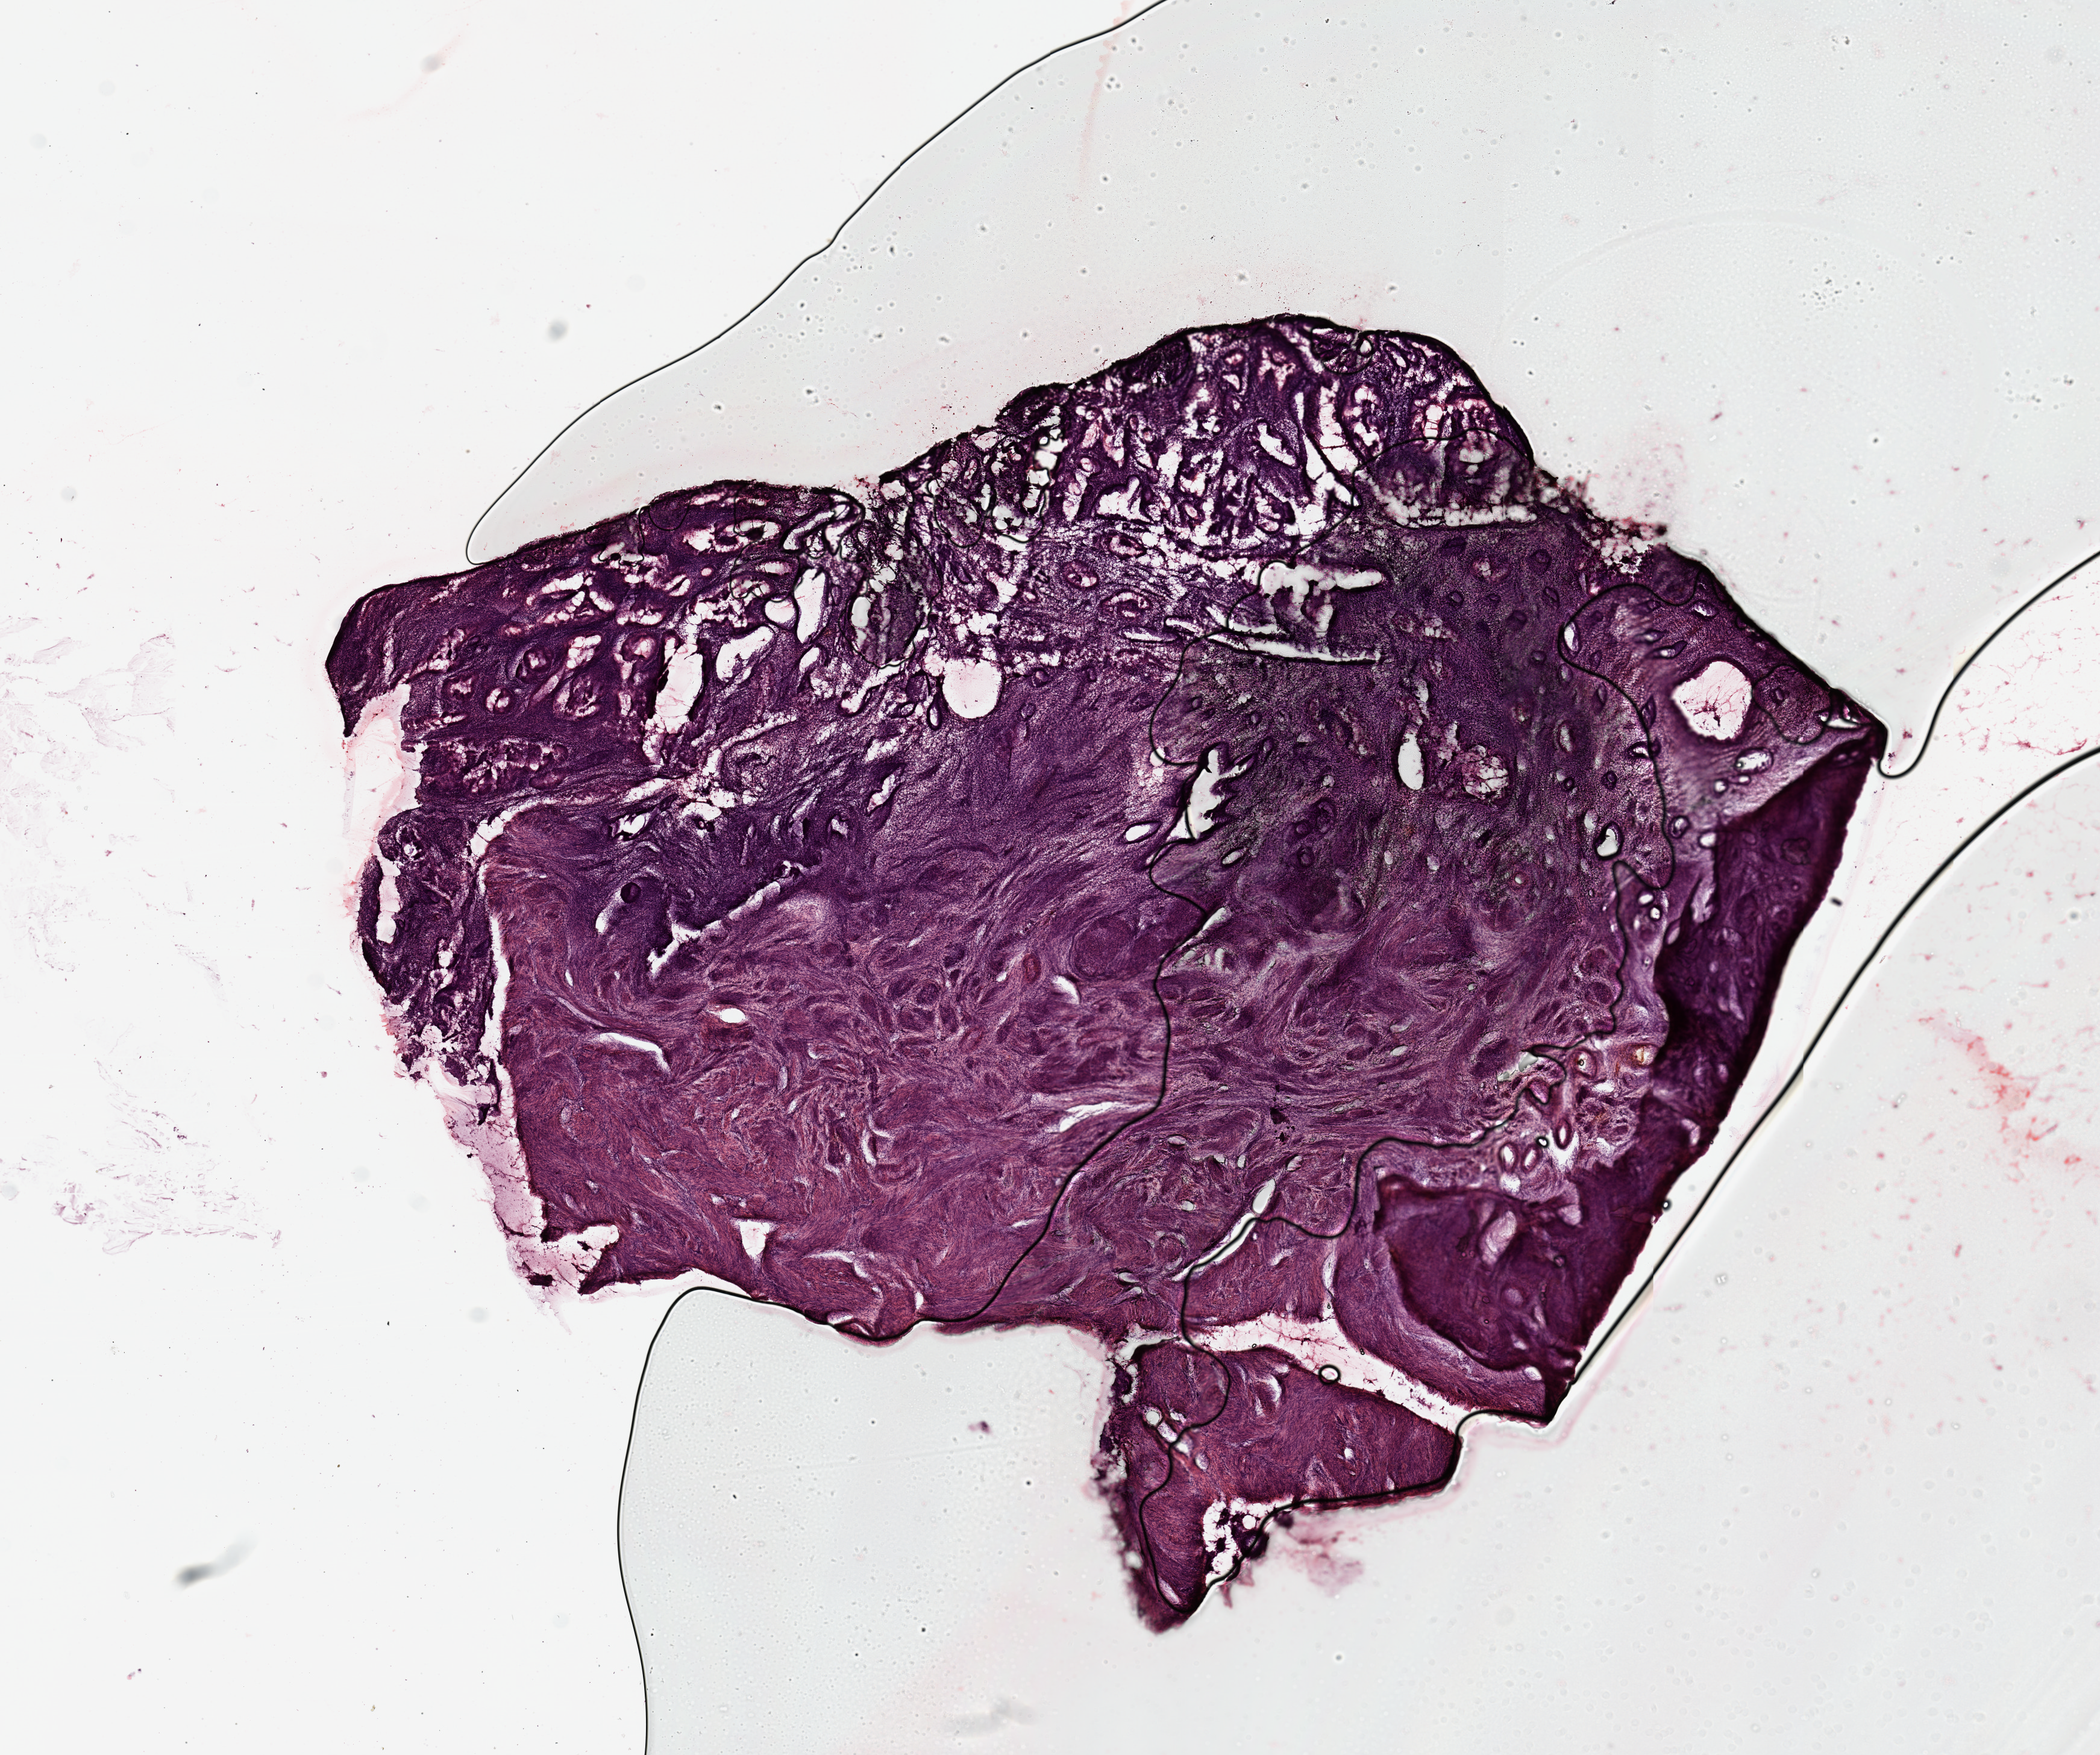
Whole-slide histology image, H&E — whole scanned area (about 13.8 x 11.5 mm) shown as a low-resolution overview, tumour tissue sample, uterus. Female, 45 y/o. Histologic grade: G1 (well differentiated).
• histologic diagnosis: Endometrioid adenocarcinoma, NOS
• AJCC pathologic stage: I